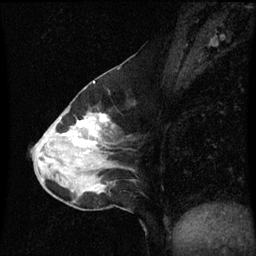
Breast MRI (dynamic contrast-enhanced), one sagittal slice. Slice 30 of 60 in the series (ordered by position). Dynamic contrast-enhanced series, image 2 of 3 at this slice position (ordered by acquisition). 1.5 T. TE 4.2 ms, TR 8.9 ms. 256 × 256 image matrix. Patient: female, 50 years. Case-level facts recorded for this patient, not image findings: setting: breast cancer imaged before/during neoadjuvant chemotherapy; receptor status: HR-positive, HER2-negative.
Structures marked on this image (semi-automatically segmented with operator editing):
- analysis volume of interest (the breast-tissue region the enhancement analysis was run in; not a lesion): bounding box [x1, y1, x2, y2] px = [34, 94, 133, 209]
- tumour enhancement mask (voxels above the 70 % enhancement threshold inside the analysis volume of interest): [68, 114, 110, 147]